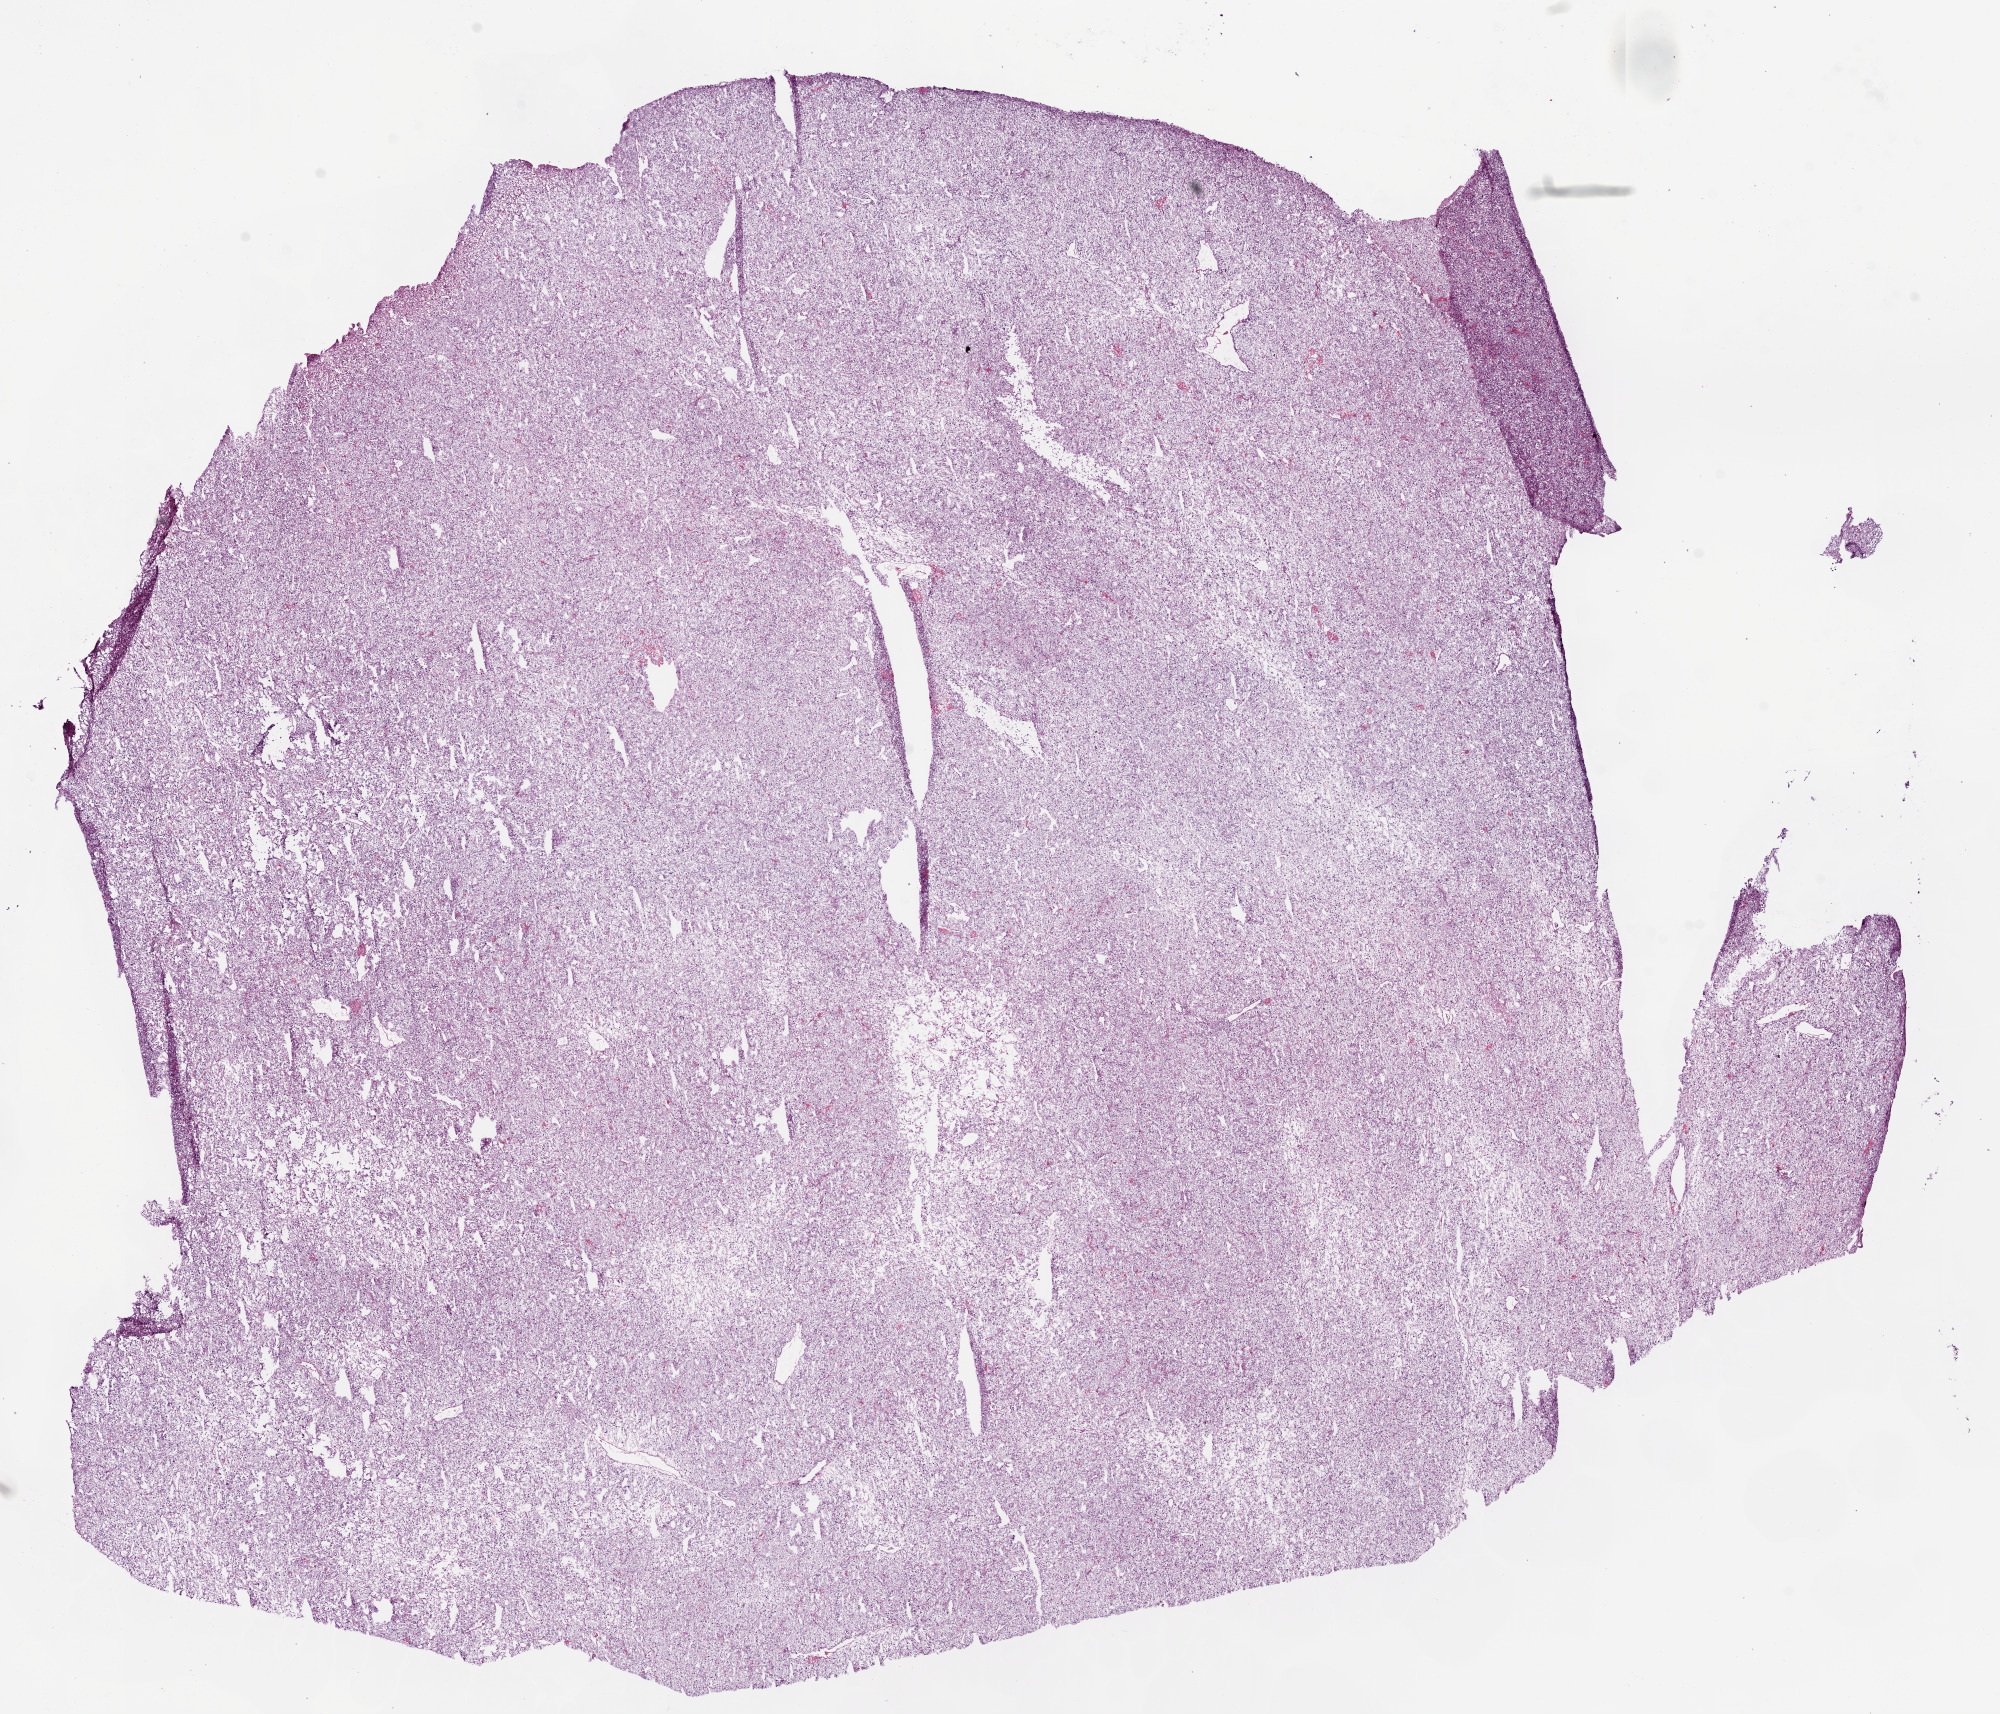
H&E-stained whole-slide image, whole scanned area (about 16.0 x 13.8 mm, from a 20x scan) shown as a low-resolution overview. Frozen section from the bottom of the tissue portion. Sample: primary tumour, kidney. Male, age 84 years at initial diagnosis.
Histologic diagnosis: Clear cell adenocarcinoma, NOS.